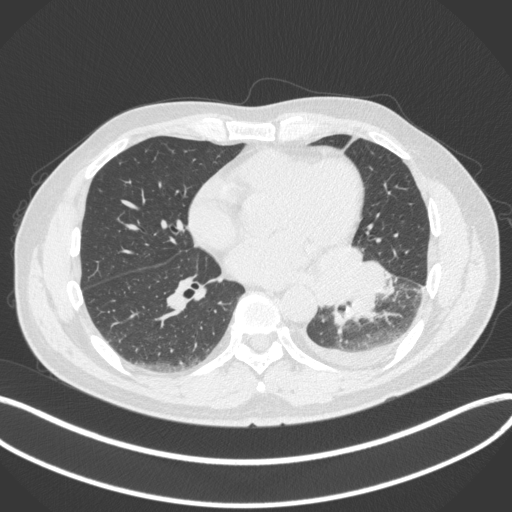
Chest CT, one axial slice. Position 154 of 350 along the scan axis. Reconstruction kernel B31f. 120 kVp. Lung window (W 1500 / L -600 HU). 1 mm slice thickness. 512 × 512 image matrix, field of view 400 × 400 mm. Patient: male, 58 years. From the clinical record (not read from this slice): clinical TNM (as recorded): T3 N1 M1b; histopathological grade: G3.
Structures marked on this image (rectangle marked by the reading radiologist):
- lung tumour (recorded histology: small cell carcinoma): bounding box <314,243,390,328> (left, top, right, bottom; pixels)